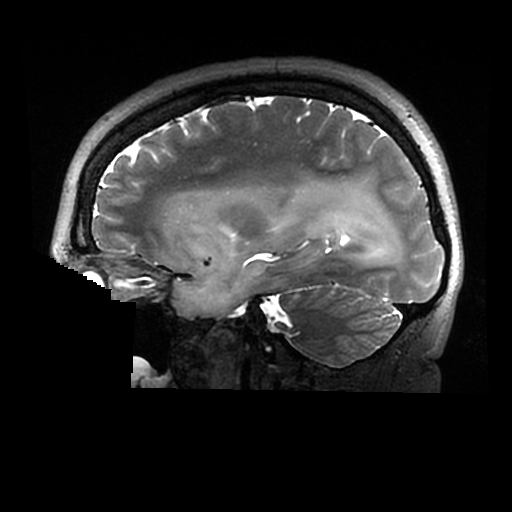
Brain MRI from a brain-tumour surgery series, one sagittal slice. Slice 196 of 320 in the series (ordered by position). 0.6 mm slice thickness. 512 × 512 image matrix, field of view 240 × 240 mm. From the clinical record (not read from this slice): histopathology: Astrocytoma; WHO grade: 2; IDH mutation: yes.
Annotated regions visible in this slice (expert manual segmentation):
- tumour: box from (x=172, y=183) to (x=403, y=319) px